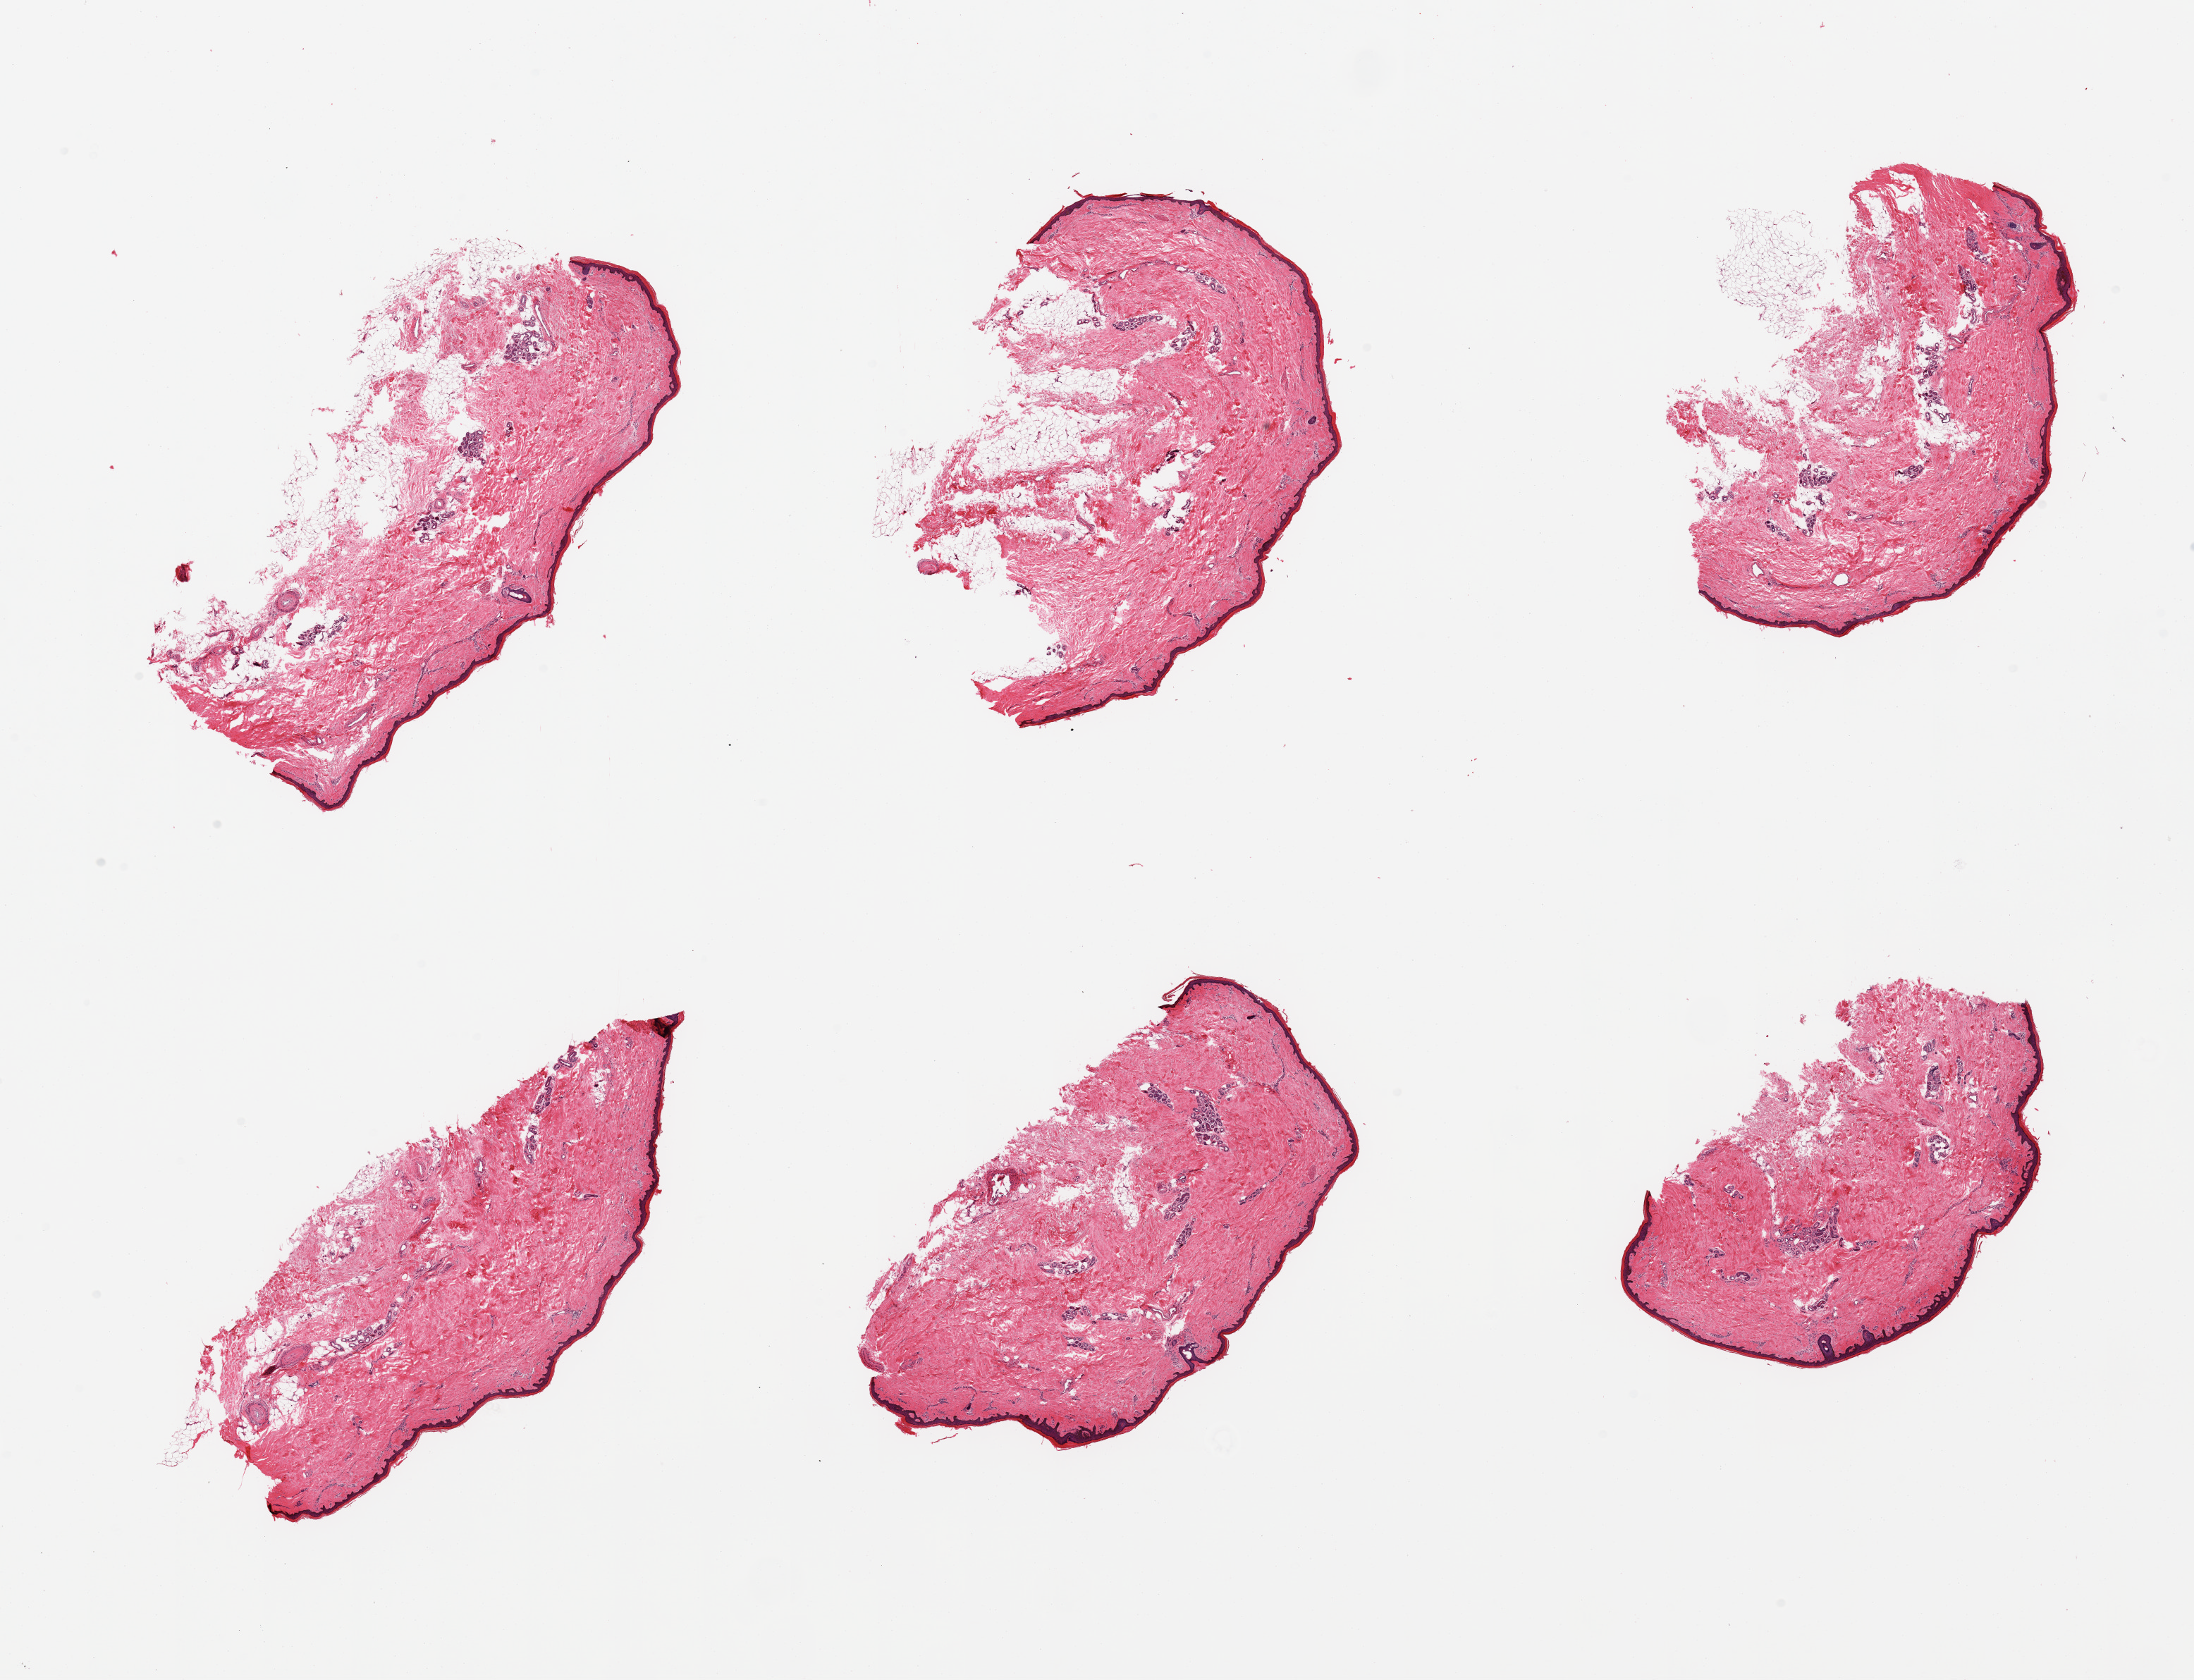
Digitized haematoxylin and eosin-stained section — whole scanned area (about 24.6 x 18.8 mm) shown as a low-resolution overview, PAXgene-fixed, paraffin-embedded tissue, target tissue: skin of lower leg, donor tissue sample.
- reviewer comment on this tissue sample: 6 pieces; 10% dermal fat